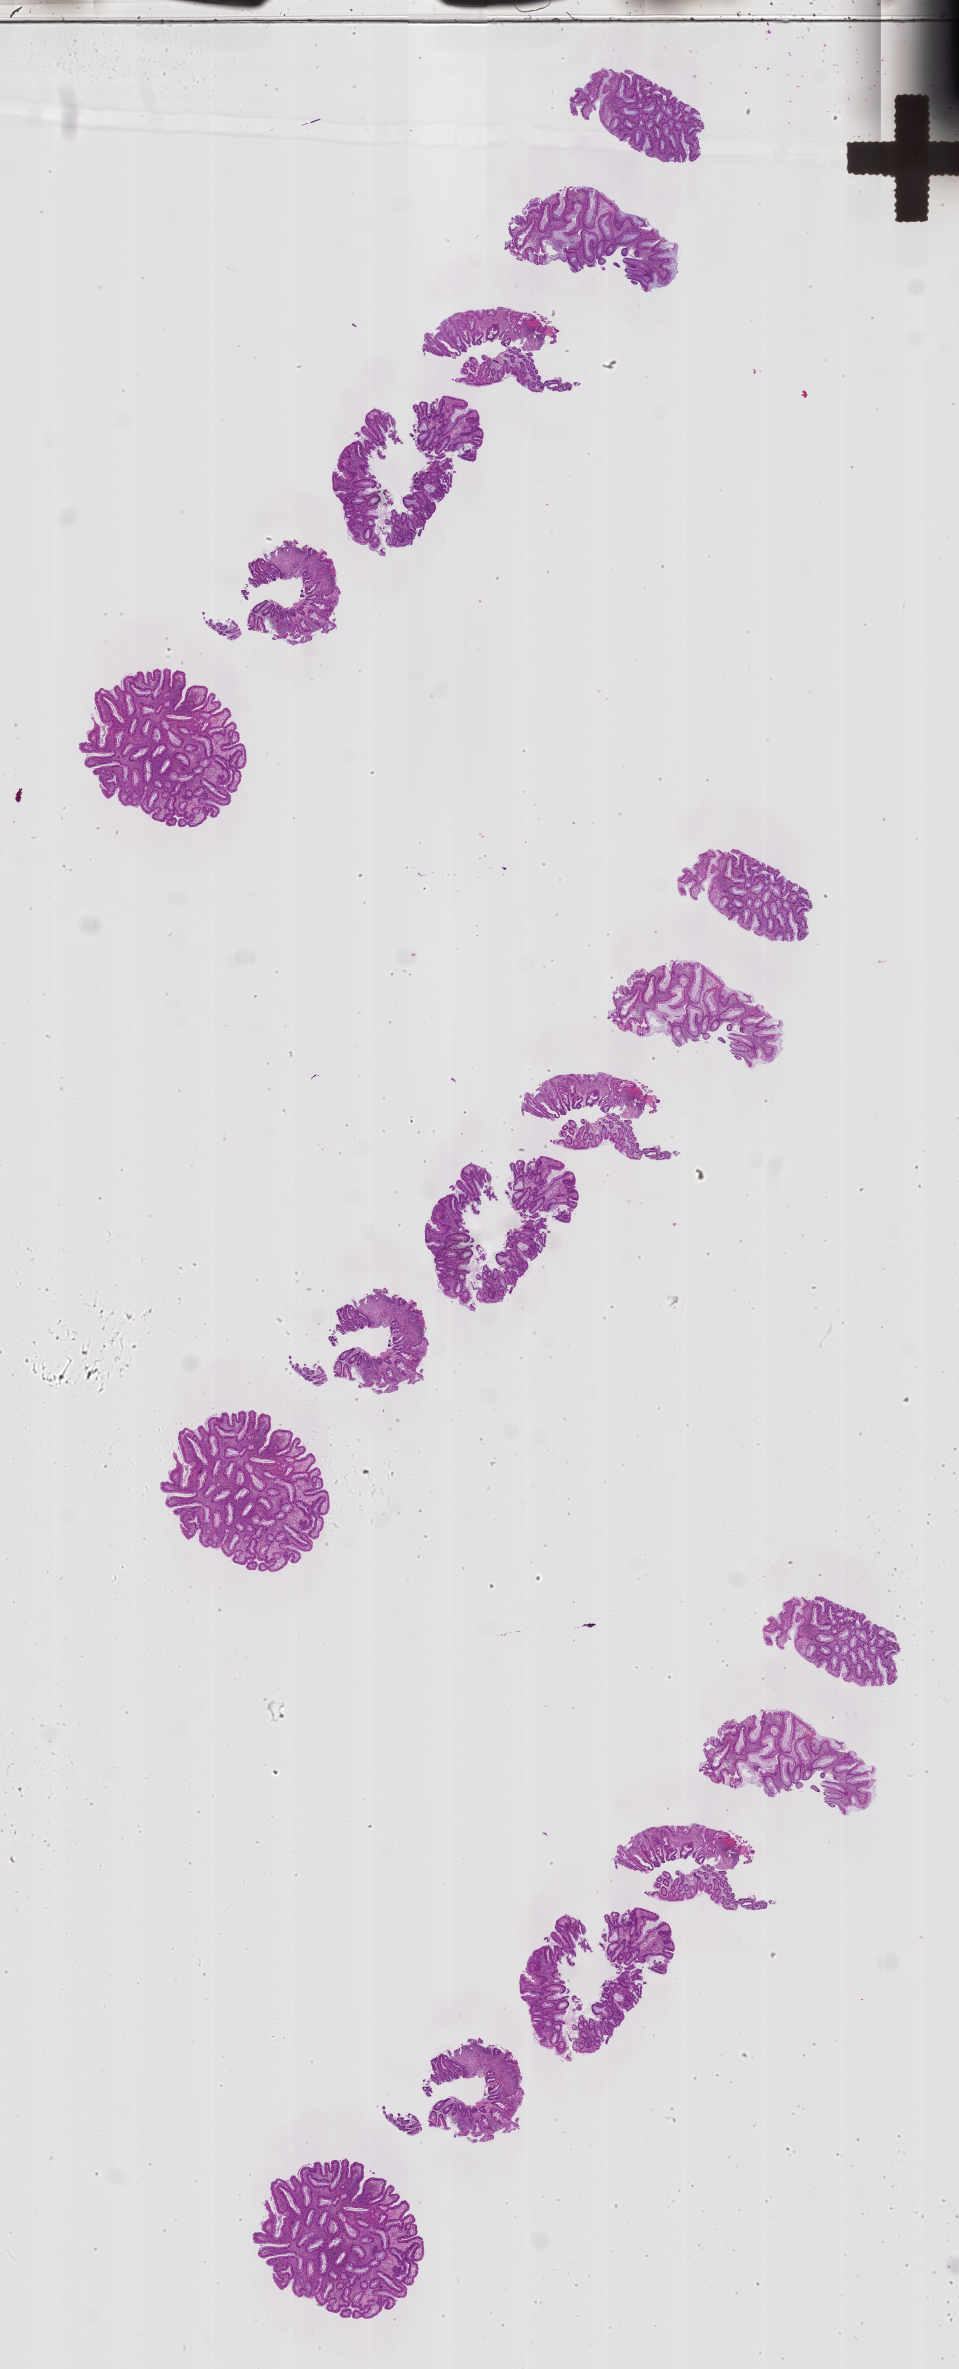
Haematoxylin and eosin whole-slide image of a colon biopsy, whole scanned area (about 15.3 x 37.9 mm) shown as a low-resolution overview. Patient sex: male.
Specimen: FFPE section; ascending colon.